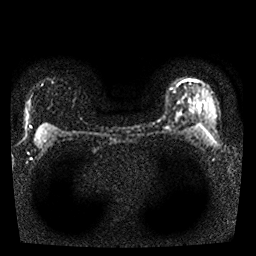
Breast MRI, one axial slice; diffusion-weighted series; image 2 of 4 stored at this slice position (different b-values; order by instance number); 1.5 T; 4 mm slice thickness; 256 × 256 image matrix, field of view 310 × 310 mm. Female patient.
Structures marked on this image (outlined manually by an expert reader):
- tumour on diffusion-weighted imaging: bounding box <165,127,170,130> (left, top, right, bottom; pixels)